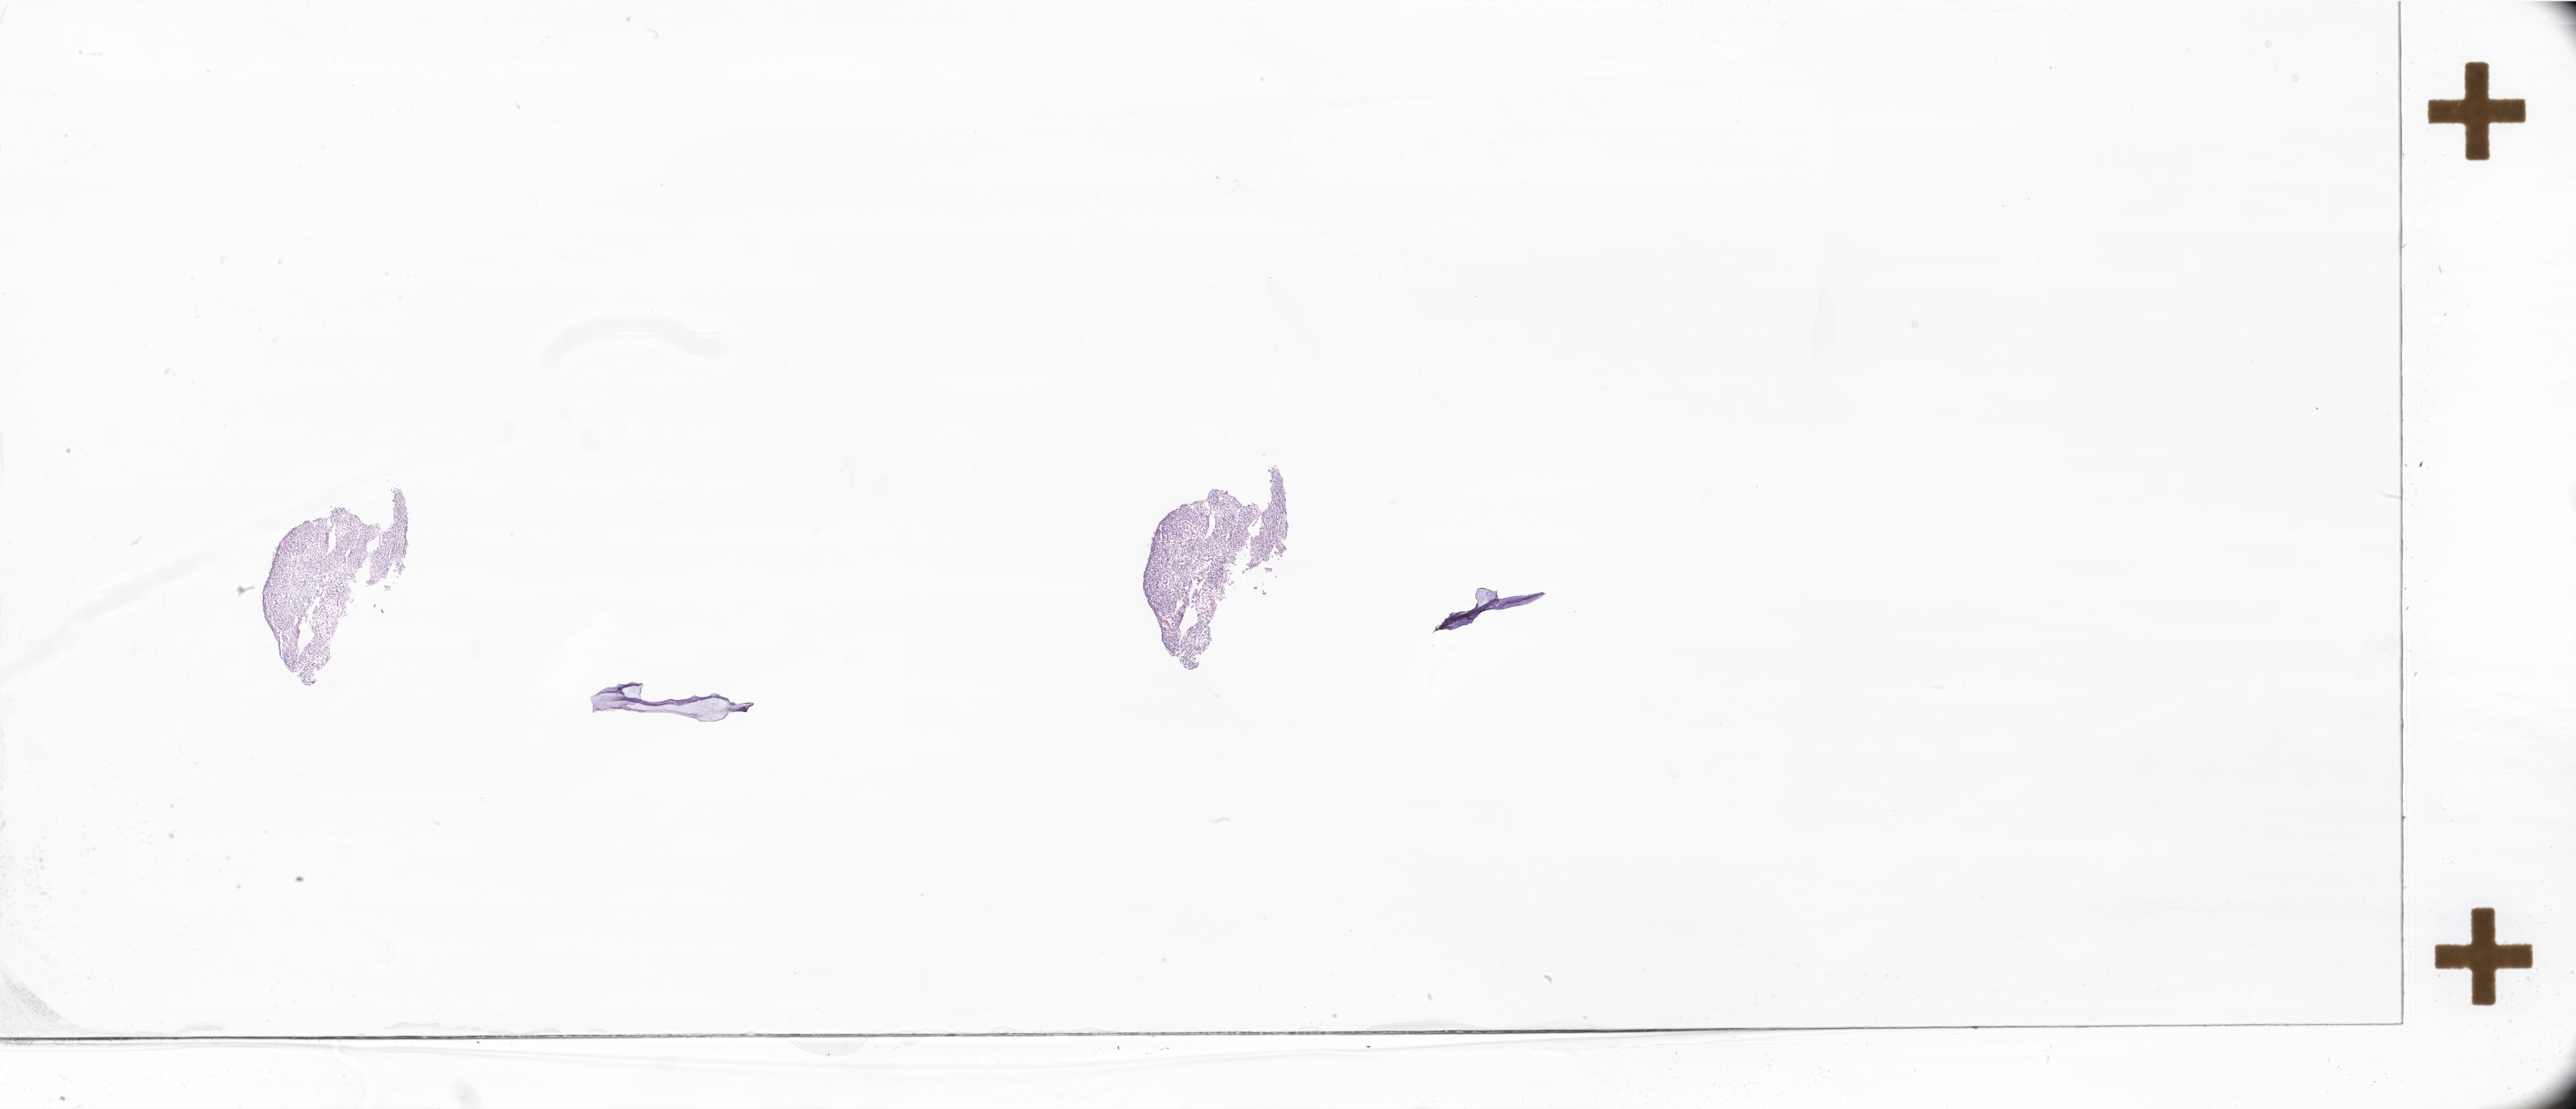
H&E whole-slide image of tumor tissue from the lower limb, a low-resolution overview of the entire scanned area, about 53.2 x 22.9 mm, frozen section (OCT-embedded). Female patient, age 867 days (about 2.4 years).
• recorded diagnosis: Alveolar rhabdomyosarcoma